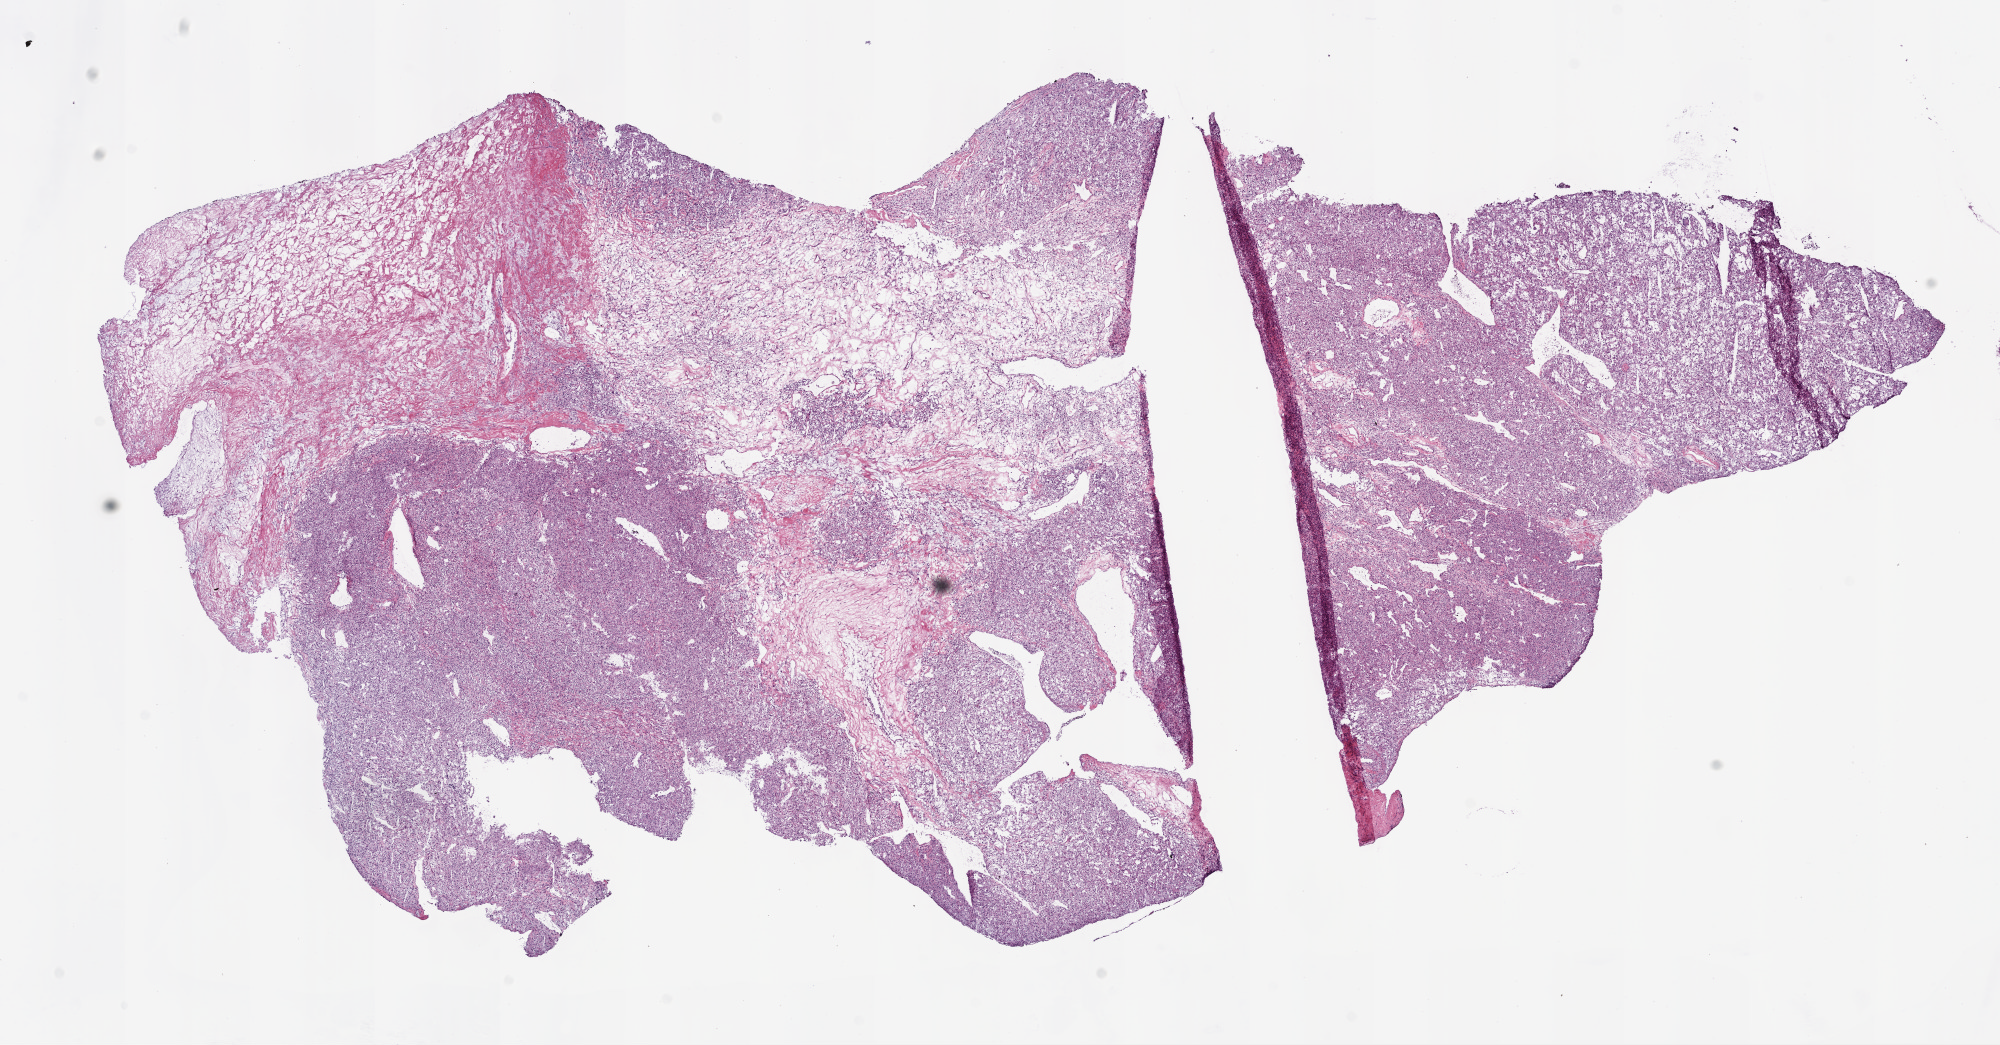
H&E-stained whole-slide image, low-resolution overview of the scanned area, about 16.0 x 8.4 mm, frozen section, sample: primary tumour, kidney. Patient: male, age at initial diagnosis 60 years. Slide review estimates, as recorded: tumour cells 70%, tumour nuclei 85%.
Histologic diagnosis: Clear cell adenocarcinoma, NOS.